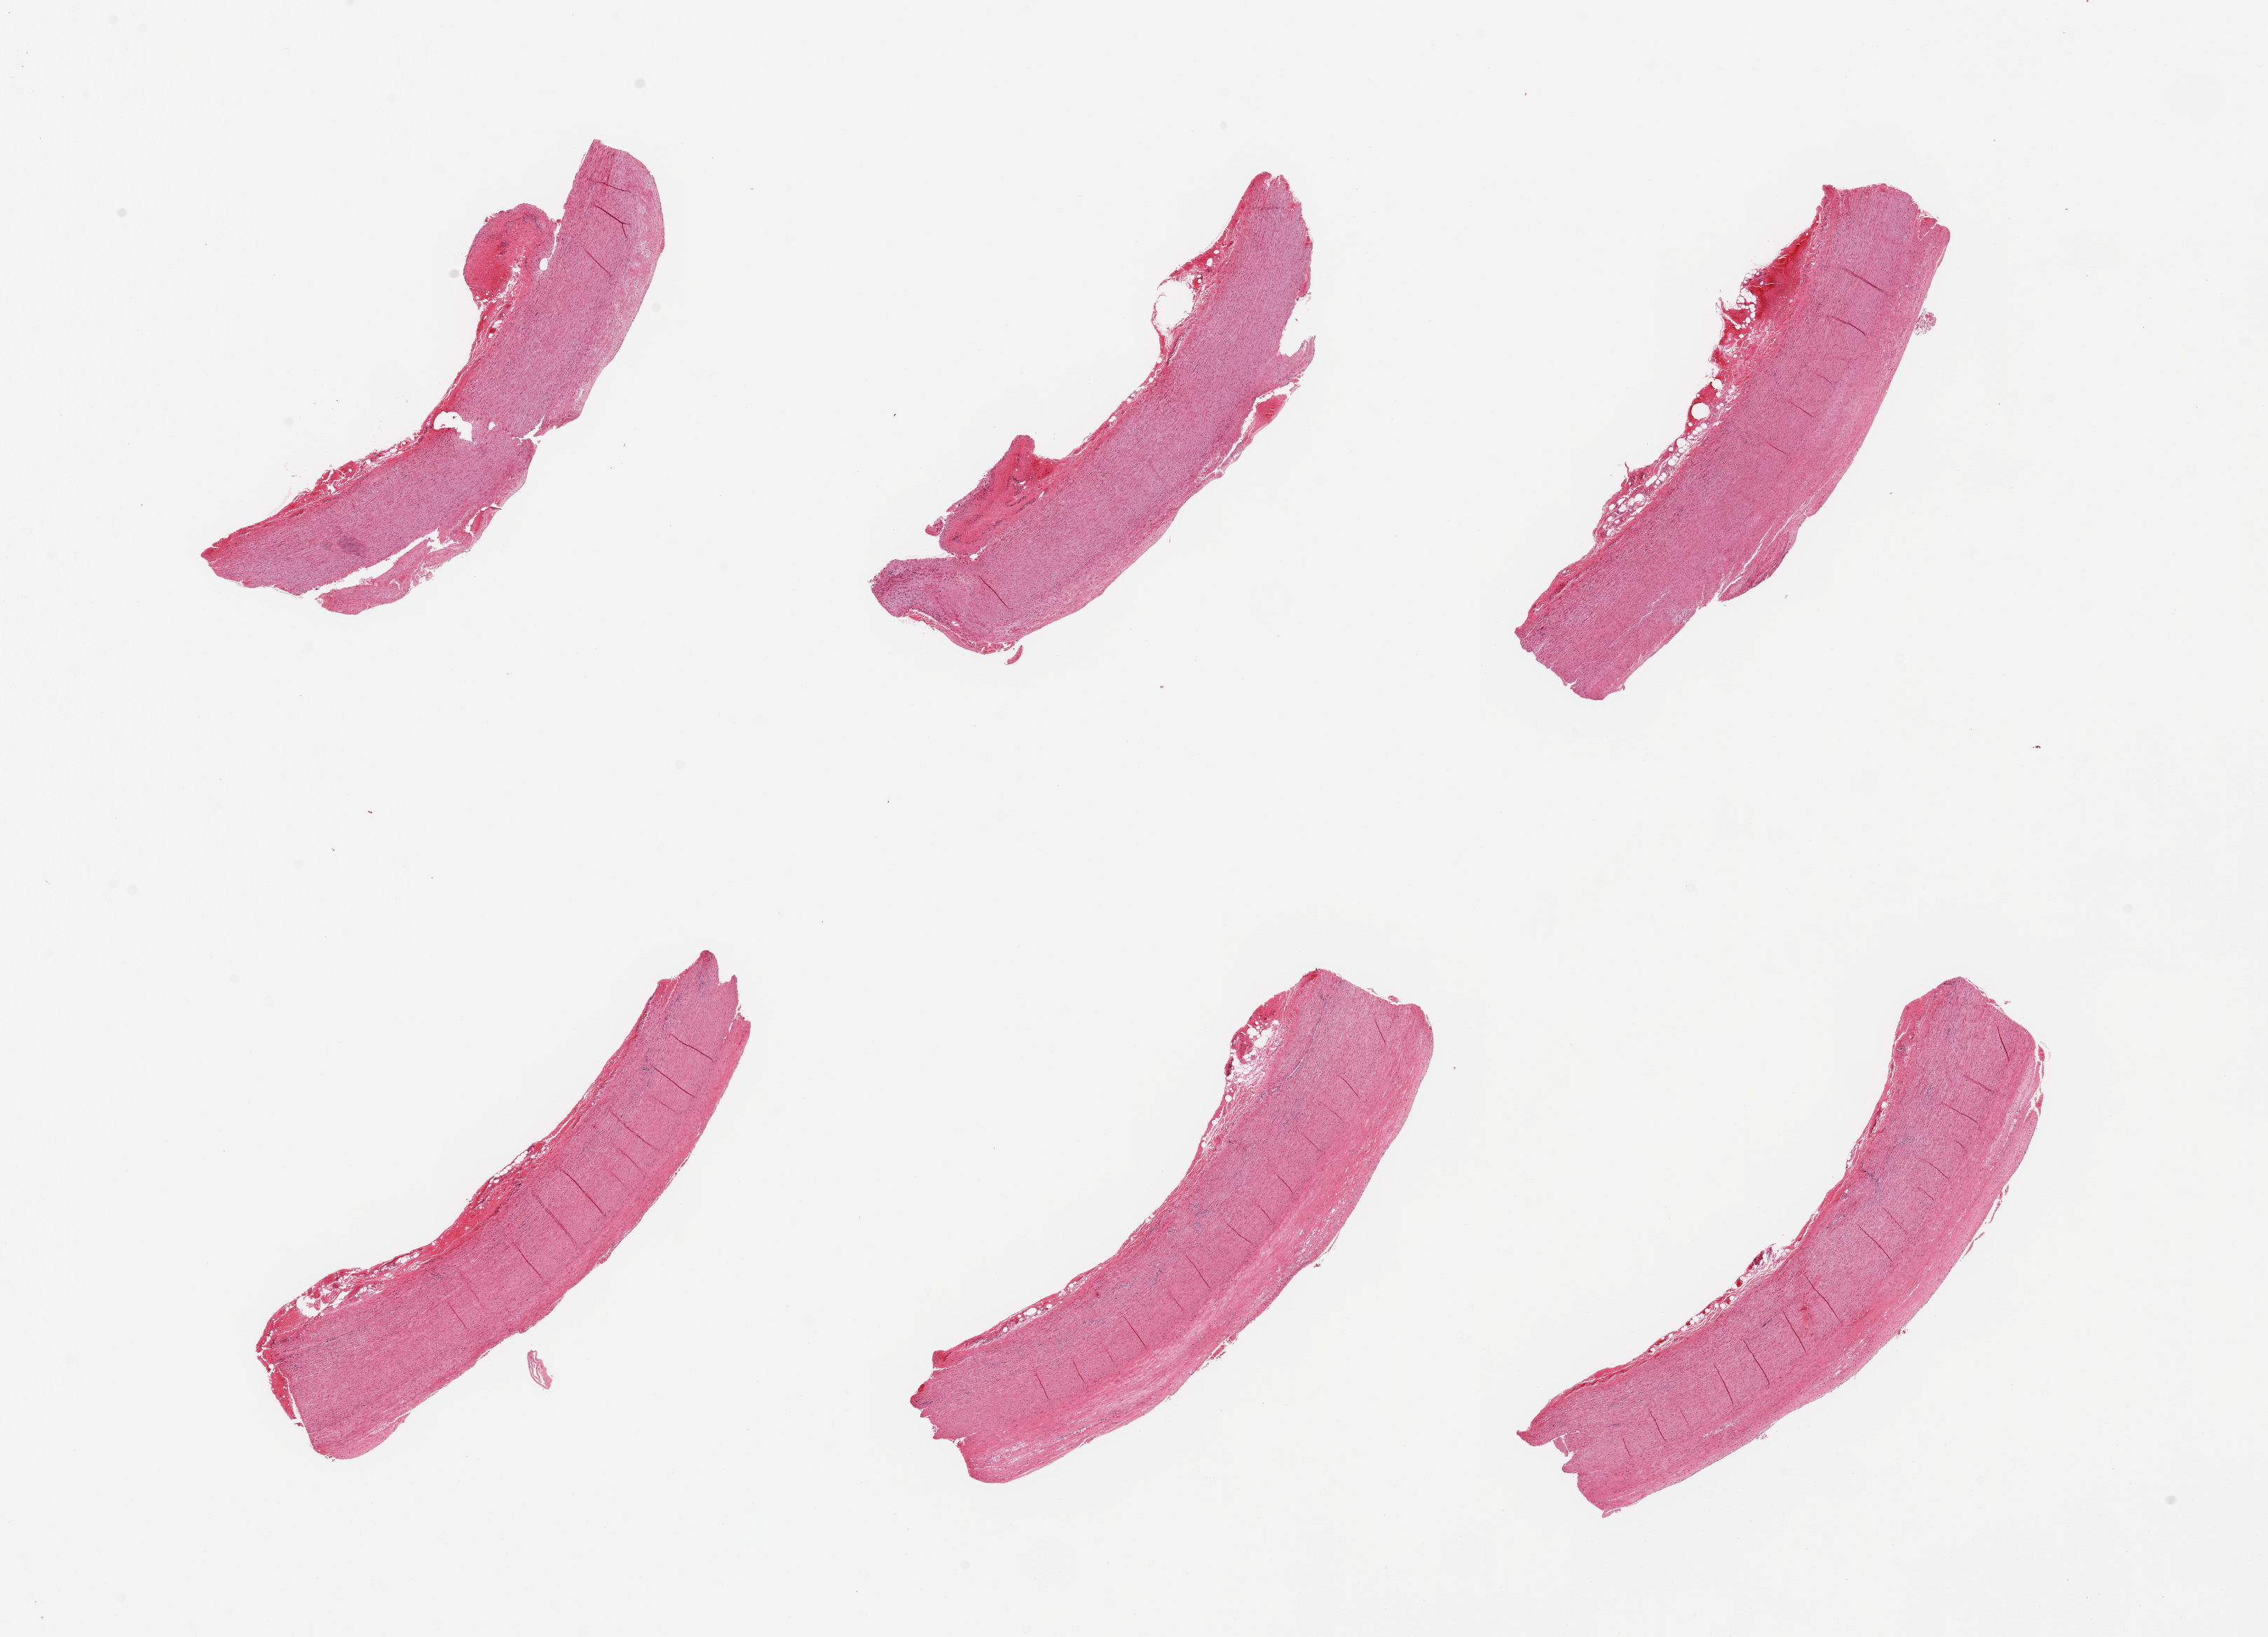
Whole-slide image, hematoxylin and eosin (H&E) stain, low-resolution overview of the scanned area, about 25.6 x 18.5 mm (acquisition: 20x scan). PAXgene-fixed paraffin-embedded (PFPE) section. Section of aorta (target tissue). Donor tissue sample. Donor: male.
- review note (as recorded): 6 pieces; atheromatous plaque